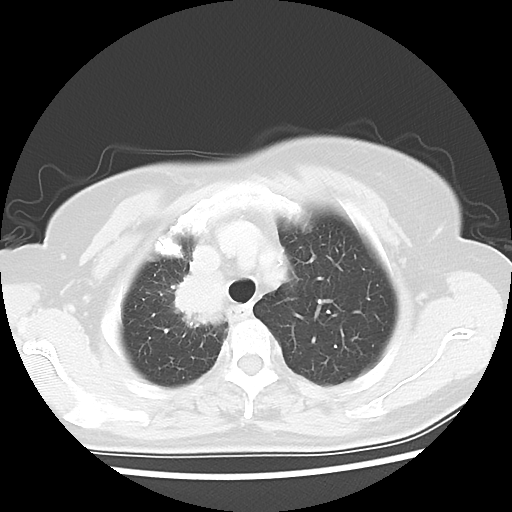
Chest CT, one axial slice; slice 46 of 56 in the series (ordered by position); reconstruction kernel LUNG; 120 kVp; lung window (W 1500 / L -600 HU); 512 × 512 image matrix, field of view 314 × 314 mm. Patient: female, 62 years. From the clinical record (not read from this slice): clinical TNM (as recorded): T2 N1 M1a.
Outlined on this slice (bounding box drawn by a radiologist):
- lung tumour (recorded histology: adenocarcinoma): bounding box (x1, y1, x2, y2) in pixels: (161, 256, 231, 336)